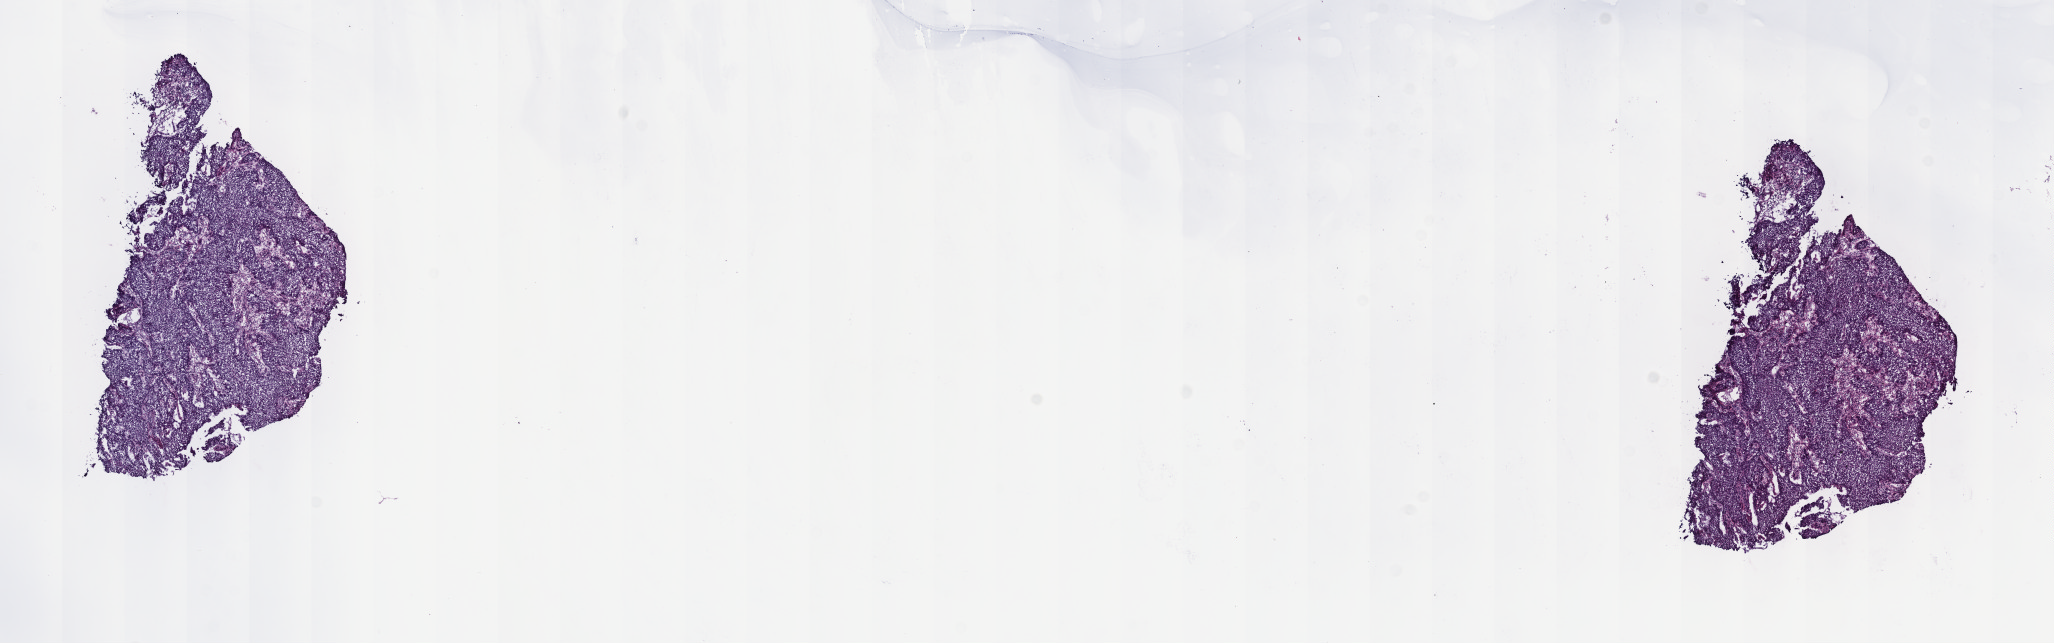
Whole-slide histology image, H&E-stained — a low-resolution overview of the entire scanned area, about 16.6 x 5.2 mm (acquisition: 40x scan), frozen section from the top of the tissue portion, sample: primary tumour, cervix. Patient: female, age at initial diagnosis 30 years. Histologic grade: G3 (poorly differentiated). Composition of this section per pathologist review: tumour cells 85%, tumour nuclei 85%, normal cells 0%, stromal cells 15%, necrosis 0%. Infiltration values recorded for this section: lymphocyte infiltration 3%, monocyte infiltration 3%, neutrophil infiltration 3%.
Histologic diagnosis: Squamous cell carcinoma, NOS.